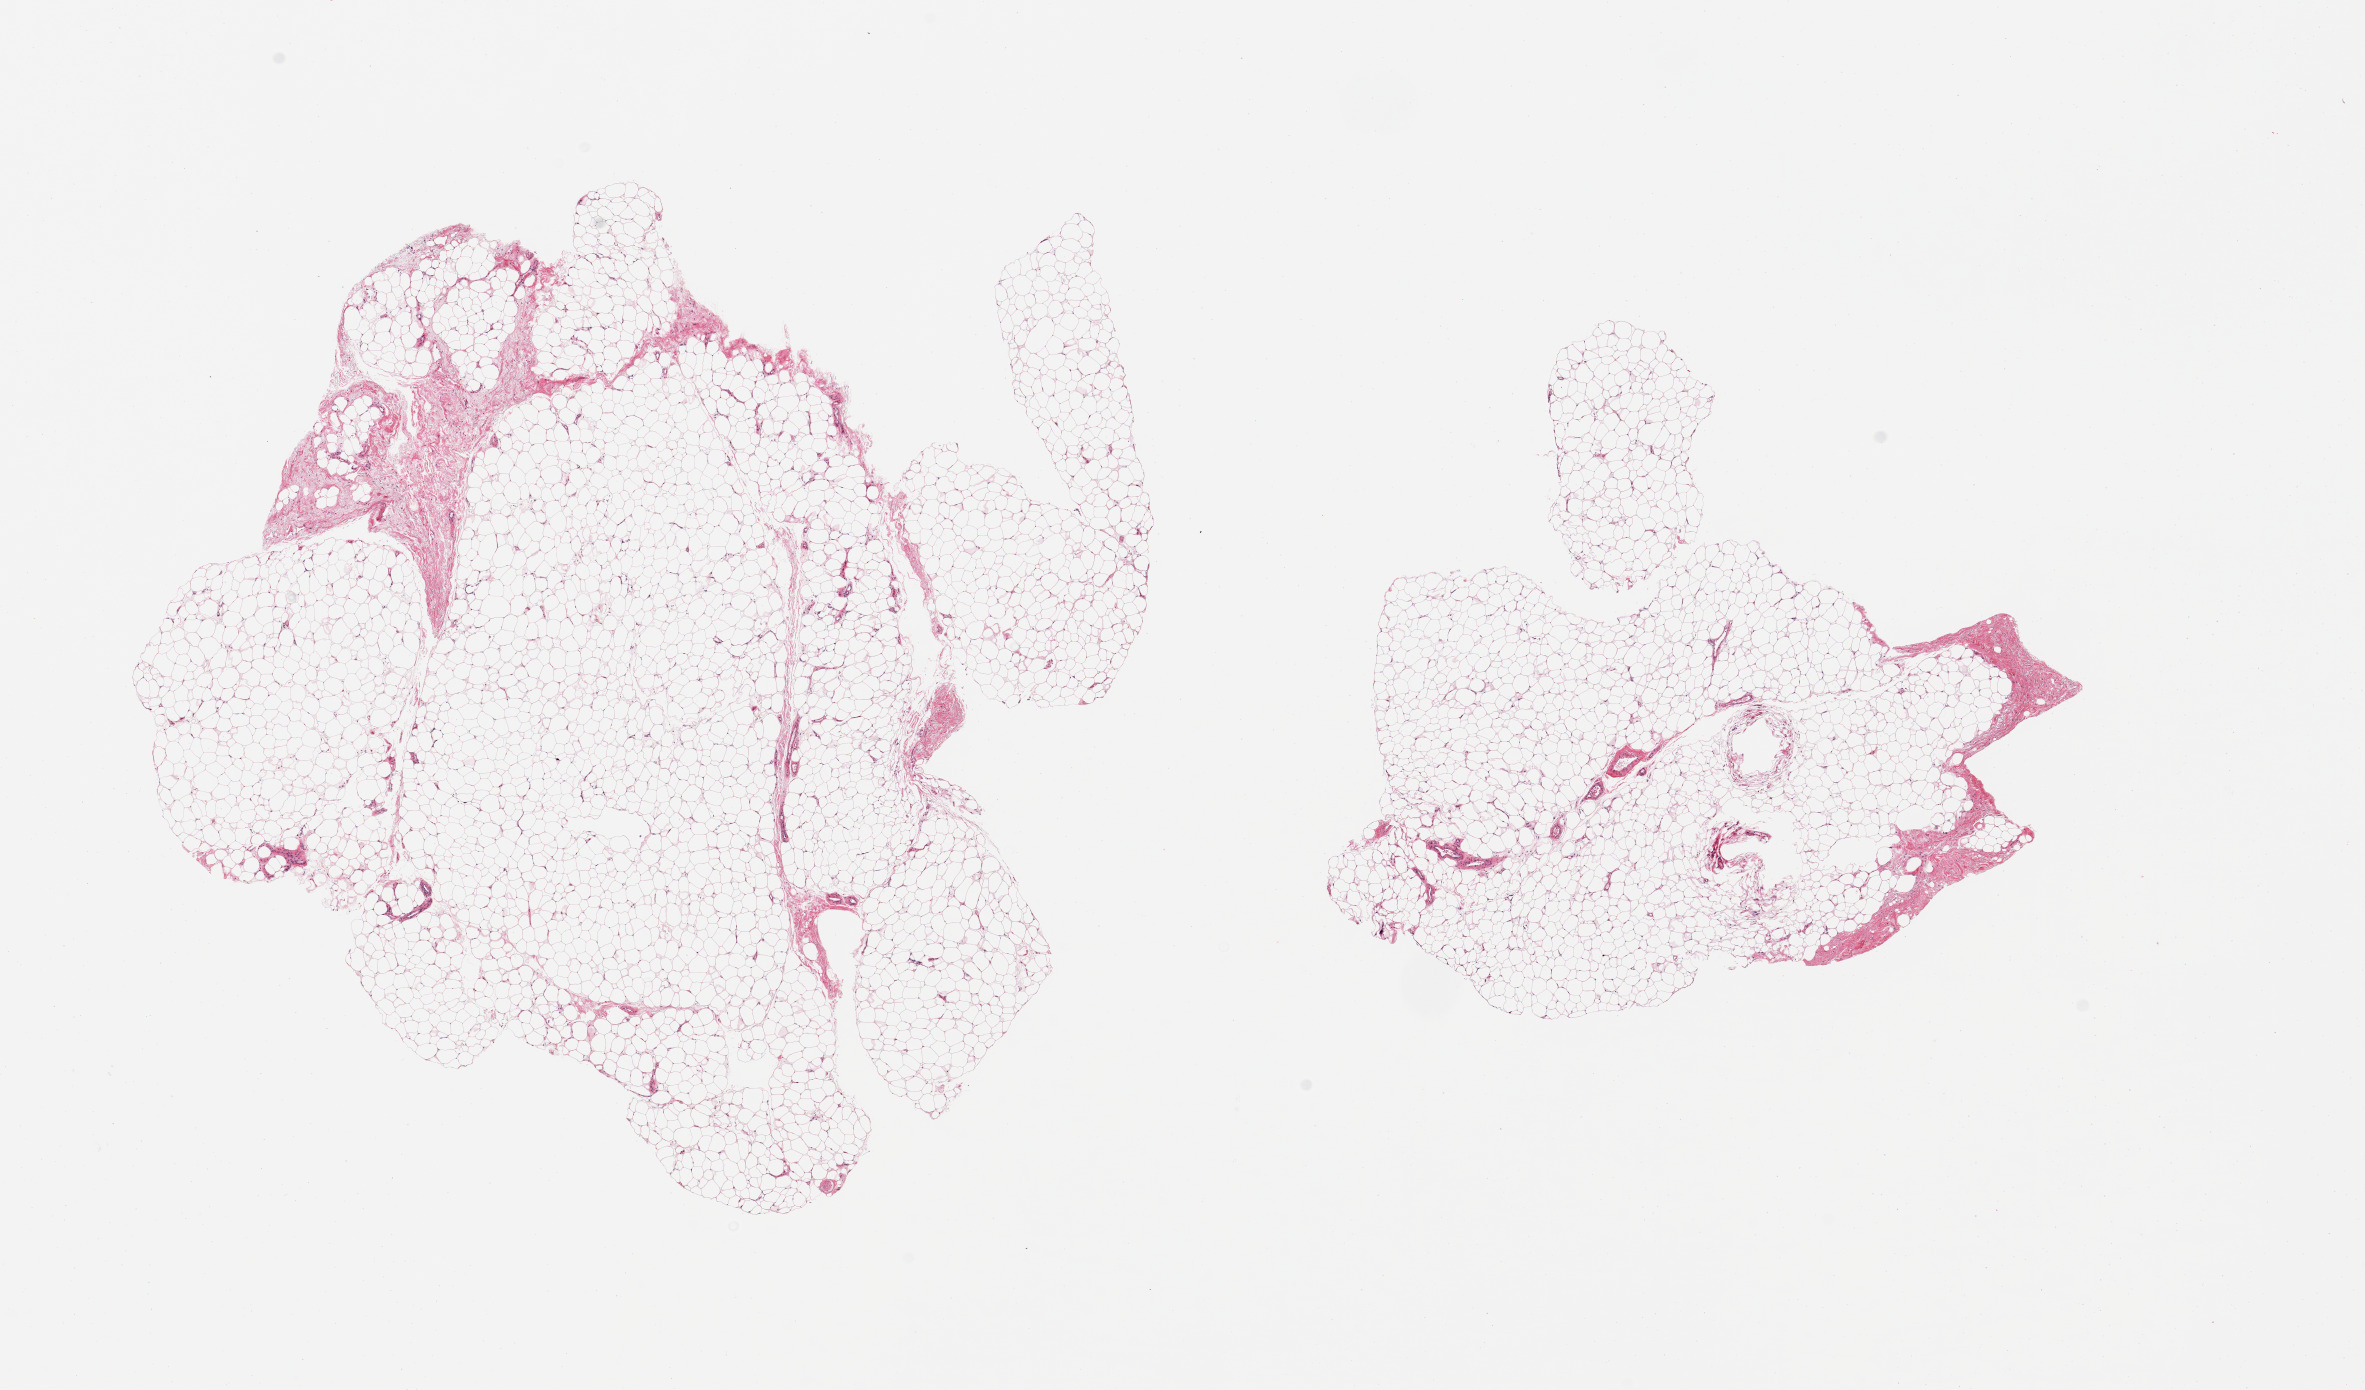
Digitized H&E-stained section, low-resolution overview of the scanned area, about 18.7 x 11.0 mm (slide scanned at 20x), PAXgene-fixed, paraffin-embedded tissue, sampled site (target tissue): adipose tissue, tissue donor sample. Donor: female.
• pathologist's review note for this sample: 2 pieces; ~10% fascia and vascular component